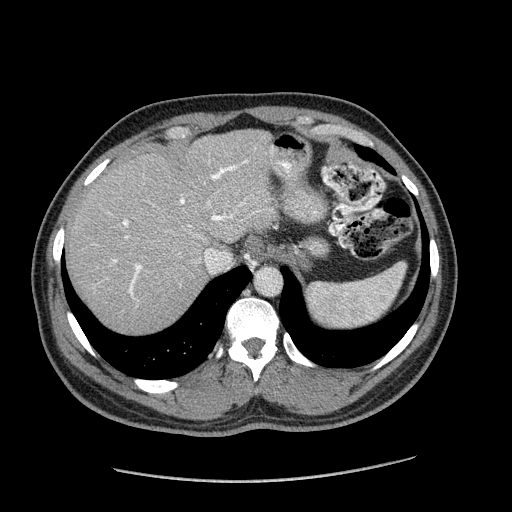
Contrast-enhanced abdominal CT (liver protocol), one axial slice; slice 143 of 182 in the series (ordered by position); reconstruction kernel STANDARD; soft-tissue window (W 400 / L 40 HU); 2.5 mm slice thickness; 512 × 512 image matrix, field of view 400 × 400 mm. From the clinical record (not read from this slice): diagnosis: hepatocellular carcinoma (patient treated with transarterial chemoembolisation; whether this scan precedes or follows treatment is not stated here); TNM stage (as recorded): Stage-I; Child-Pugh class: A; tumour differentiation: well differentiated; tumour nodularity: uninodular.
Annotated regions visible in this slice (semi-automatic segmentation, software-assisted and operator-edited):
- abdominal aorta: bounding box [x1, y1, x2, y2] px = [256, 268, 281, 295]
- liver parenchyma outside the tumour (the mass and vessels are separate outlines, so this box may not span the whole liver): [66, 130, 276, 332]
- liver vessels: [112, 161, 247, 295]